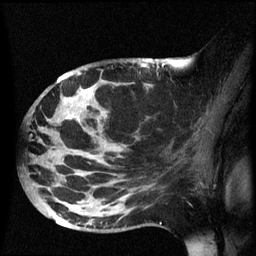
Breast MRI (dynamic contrast-enhanced), one sagittal slice. Slice 36 of 60 in the series (ordered by position). Dynamic contrast-enhanced series, image 2 of 3 at this slice position (ordered by acquisition). 1.5 T. TE 4.2 ms, TR 8.4 ms. 2.5 mm slice thickness. 256 × 256 image matrix, field of view 220 × 220 mm. Patient: female, 49 years.
Annotated regions visible in this slice (semi-automatically segmented with operator editing):
- analysis volume of interest (the breast-tissue region the enhancement analysis was run in; not a lesion): bounding box (x1, y1, x2, y2) in pixels: (25, 72, 164, 233)
- tumour enhancement mask (voxels above the 70 % enhancement threshold inside the analysis volume of interest): (67, 116, 76, 119)